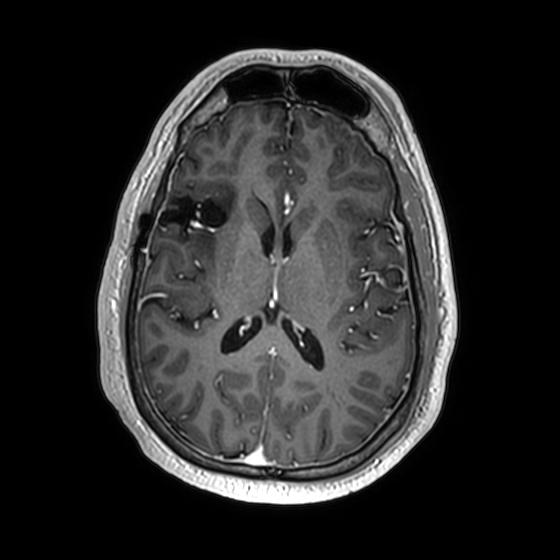
Brain MRI from a brain-tumour surgery series, one axial slice; slice 82 of 174 in the series (ordered by position); T1-weighted post-contrast; 1 mm slice thickness; 560 × 560 image matrix. From the clinical record (not read from this slice): histopathology: Astrocytoma; WHO grade: 2; IDH mutation: yes; tumour location: Right Insular.
Annotated regions visible in this slice (expert manual segmentation):
- previous resection cavity: bounding box [x1, y1, x2, y2] px = [159, 196, 227, 227]